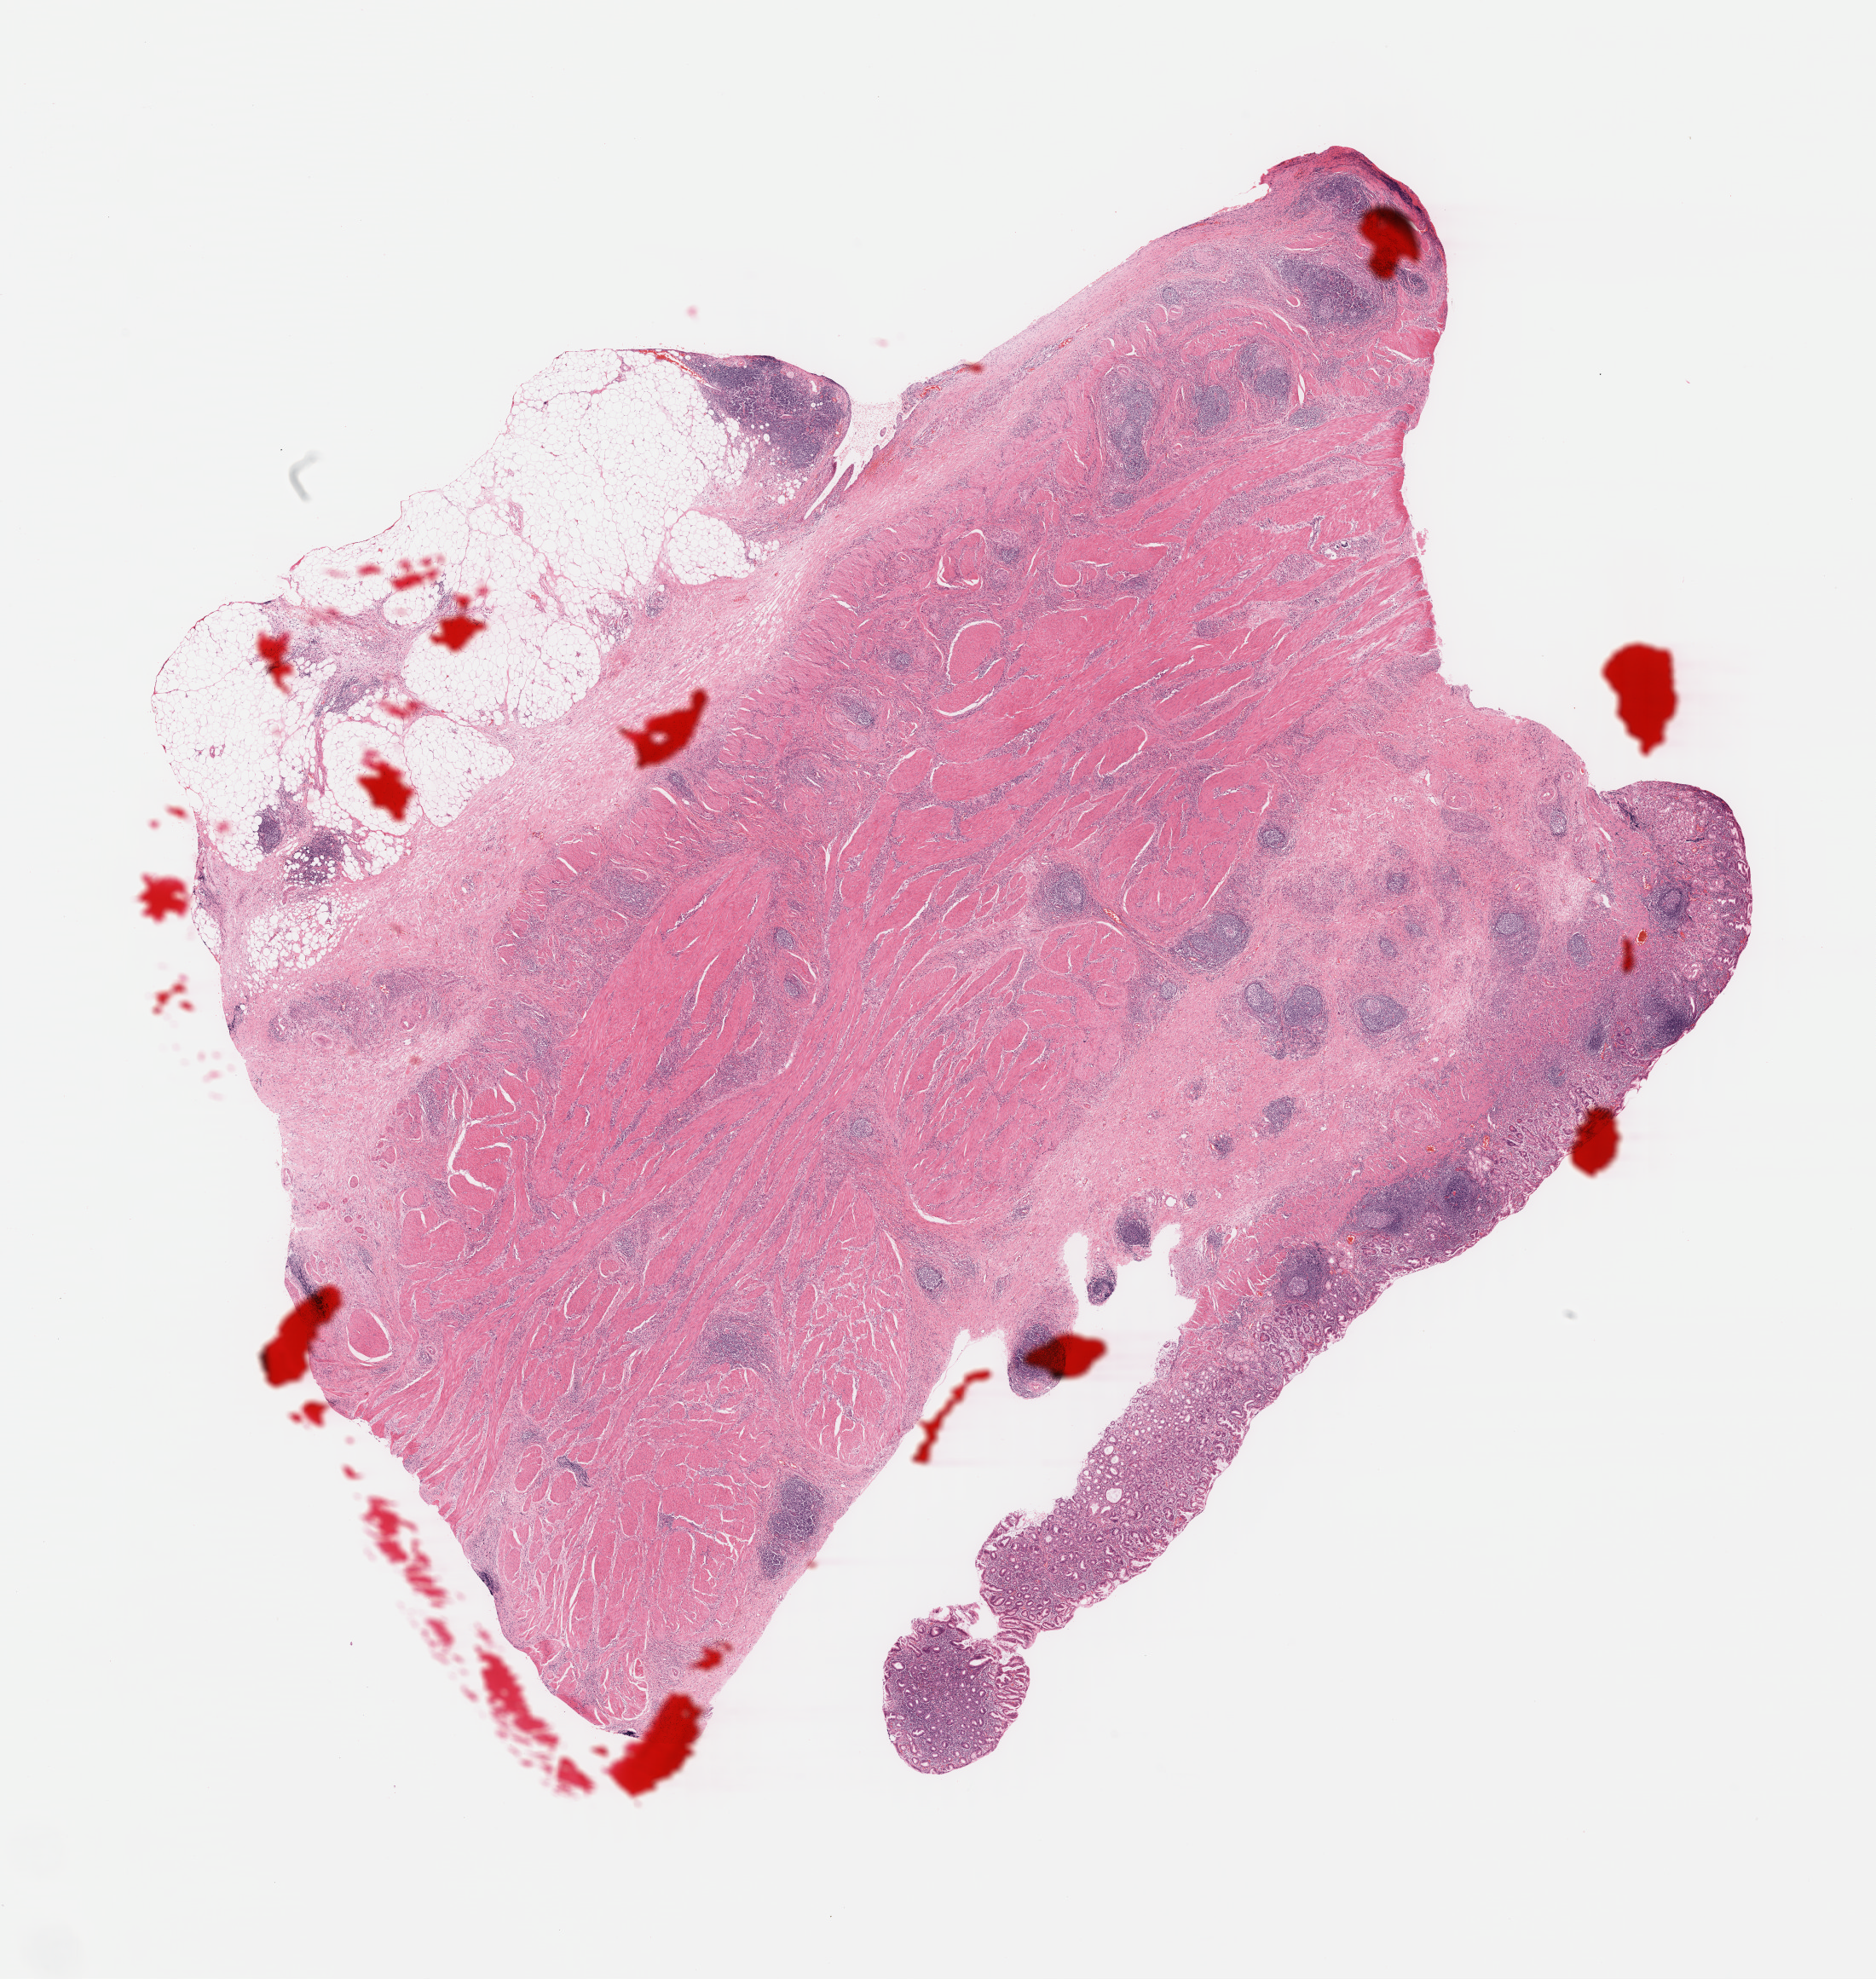
H&E whole-slide image, whole scanned area (about 17.3 x 18.3 mm) shown as a low-resolution overview. Formalin-fixed paraffin-embedded (FFPE) diagnostic section. Sample: primary tumour, stomach. Female, age 53 years at initial diagnosis. Histologic grade: G3 (poorly differentiated).
- pathologic diagnosis: Carcinoma, diffuse type (cardia, NOS)
- AJCC pathologic stage: IIA